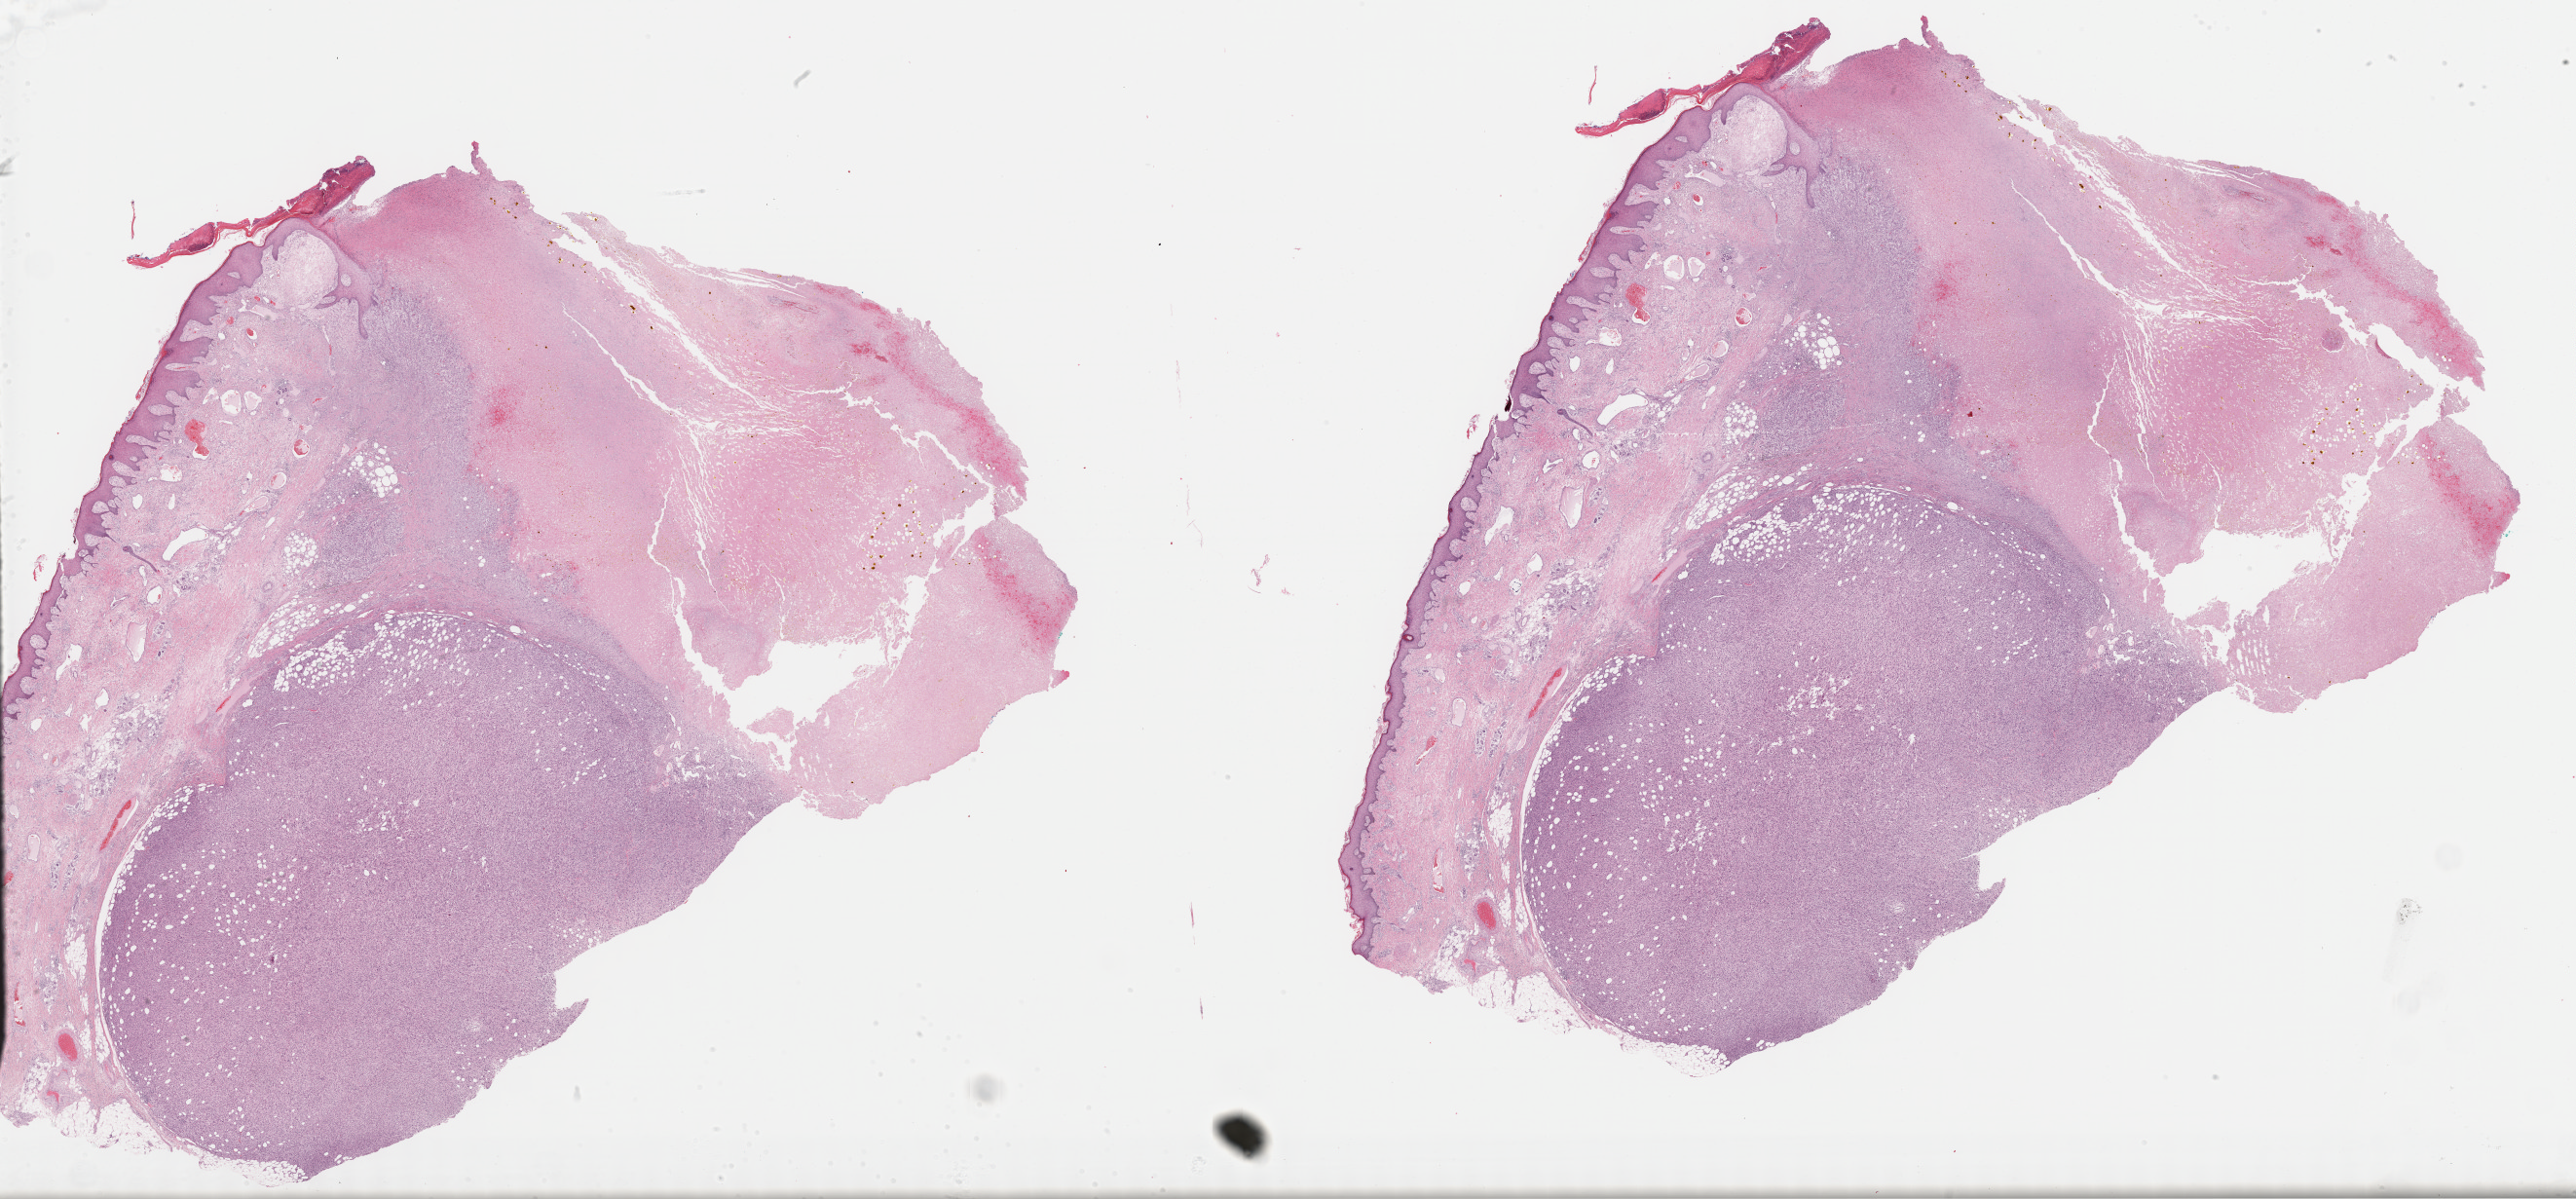
Digitized H&E-stained tissue section (whole slide) — shown as a low-resolution overview of the whole scanned area (about 42.8 x 19.9 mm, from a 40x scan); FFPE section; sample: primary tumour, connective, subcutaneous and other soft tissues. Patient: female, age at initial diagnosis 65 years.
Diagnosis: Malignant fibrous histiocytoma (connective, subcutaneous and other soft tissues of lower limb and hip).